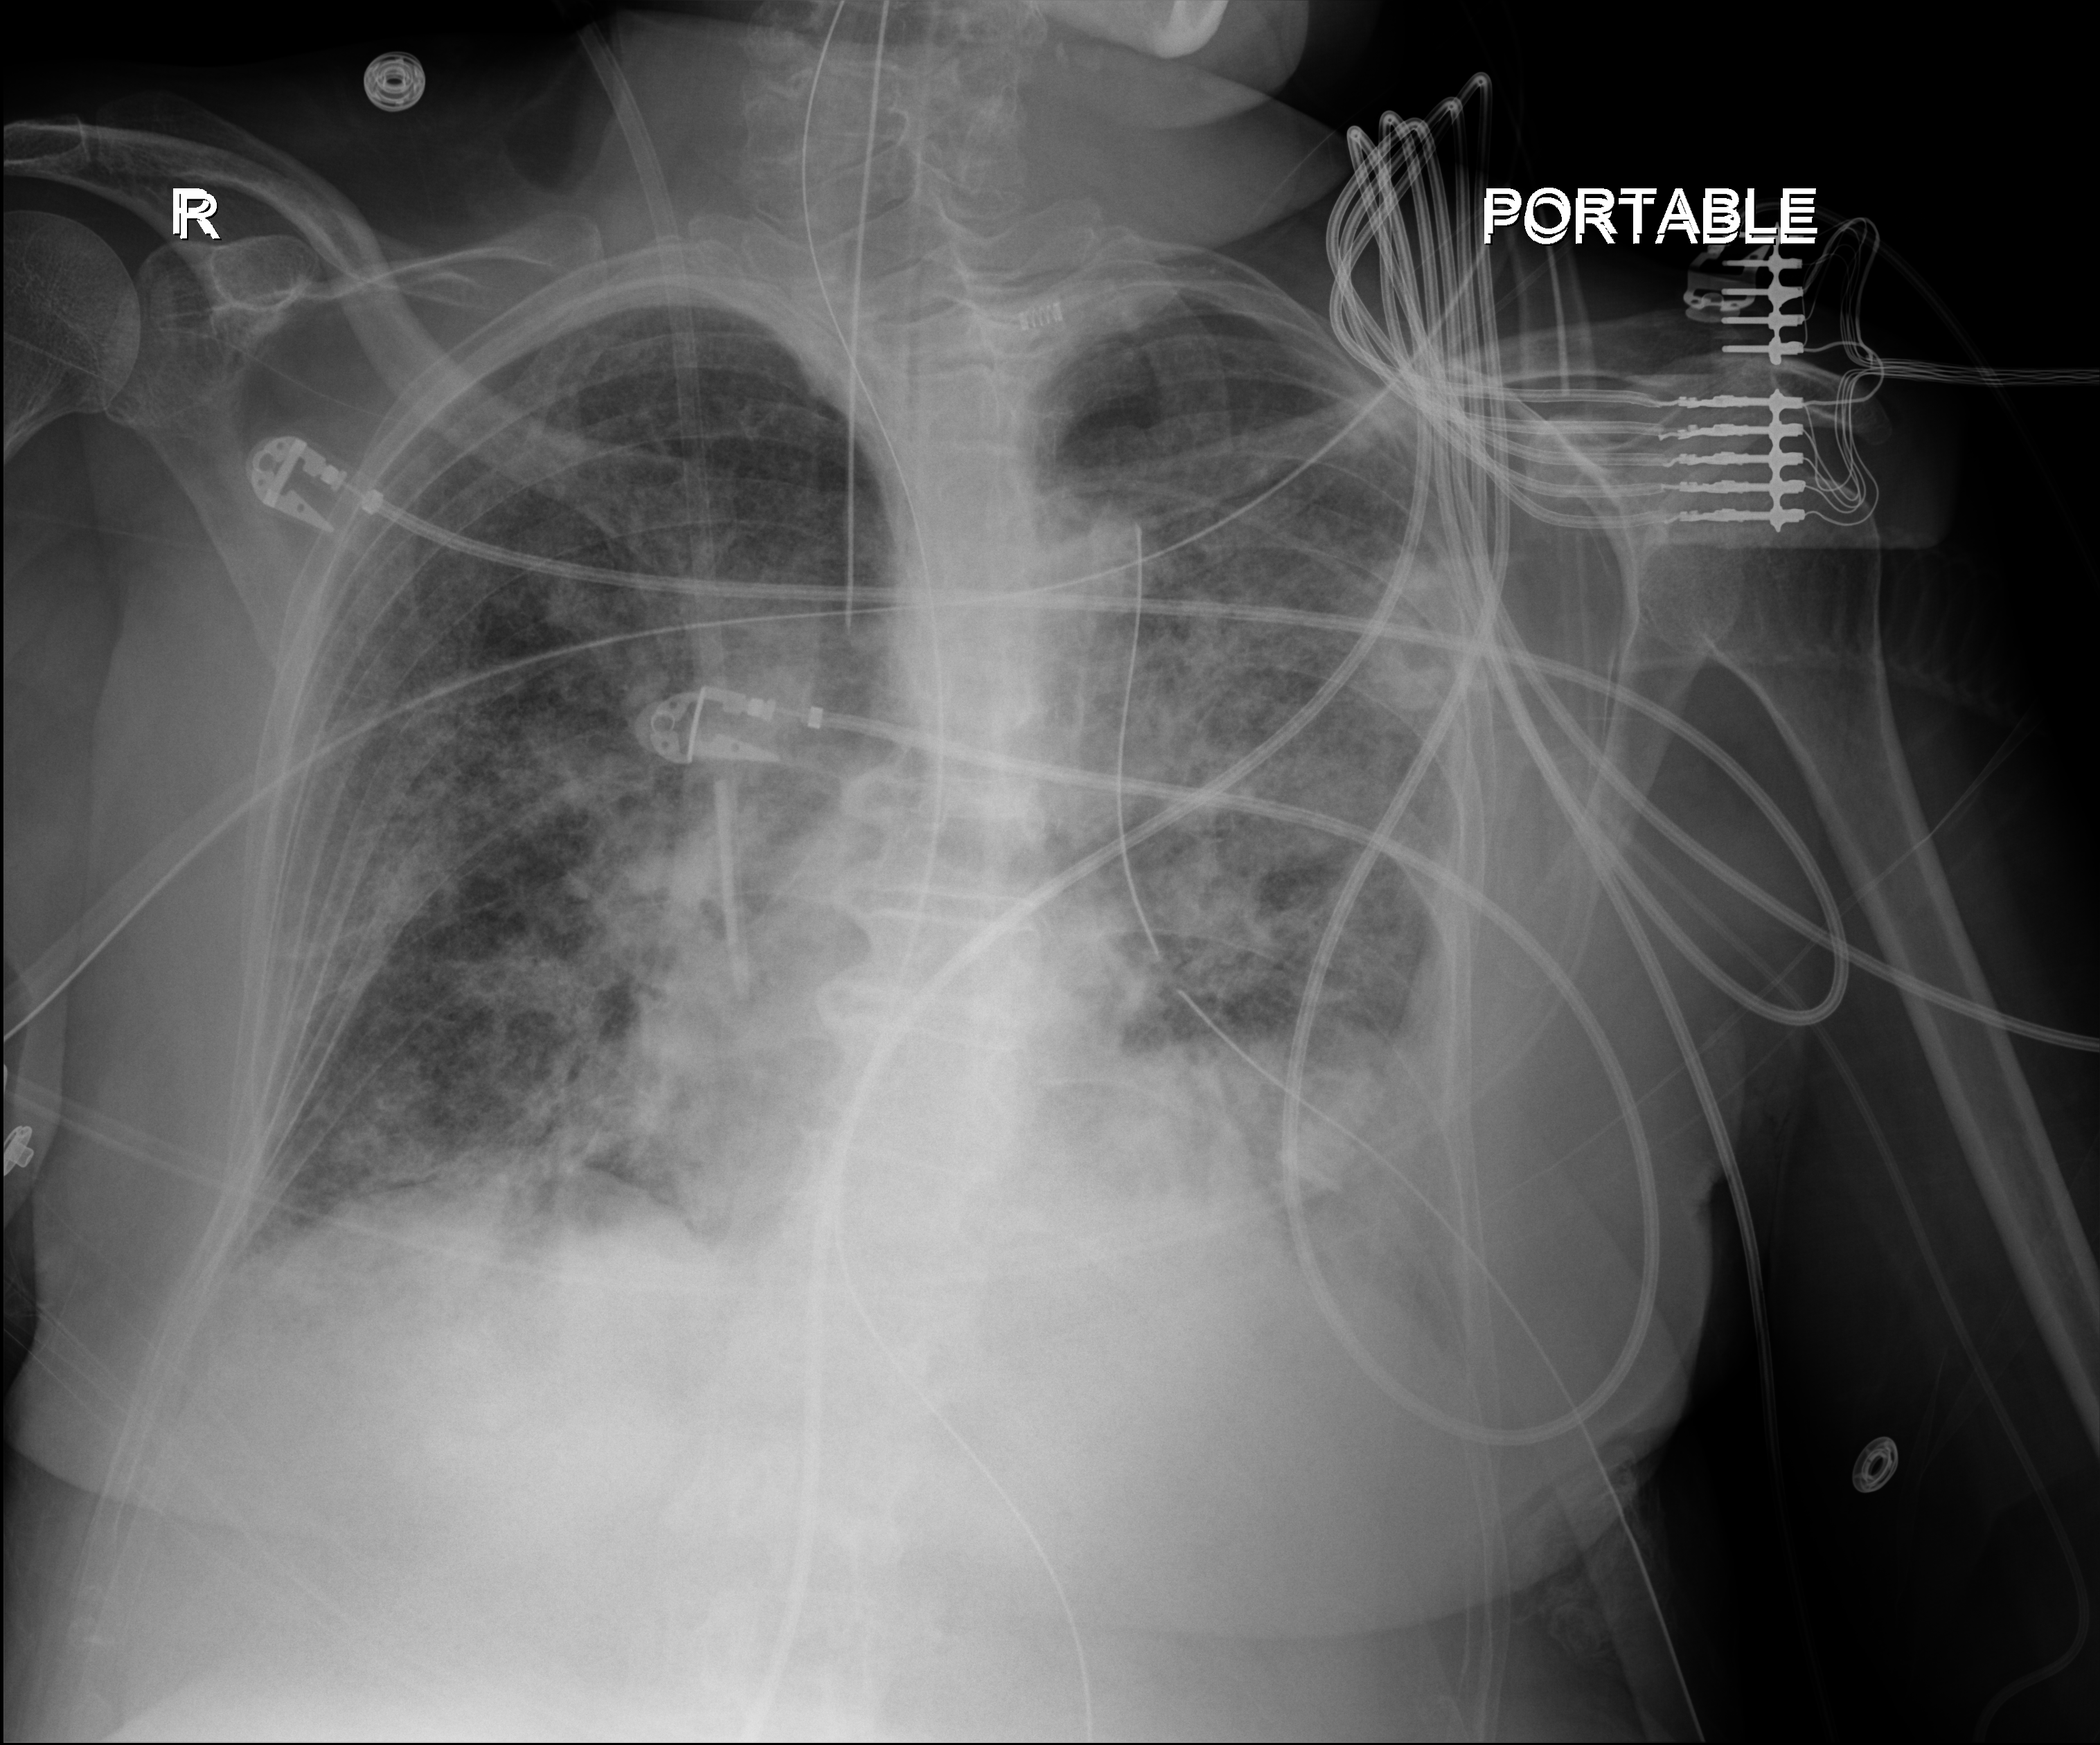
Bedside chest radiograph (digital radiography), anteroposterior (AP) projection. Patient hospitalised with COVID-19; female, aged 75–90 years.
From the hospital-stay record, not from the radiograph (when in the stay this image was taken is not recorded):
- other chronic lung disease (admission record): yes